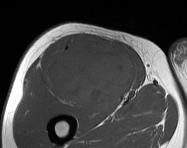
MRI of an extremity soft-tissue mass, one axial slice. Position 90 of 114 along the scan axis. MR volume resampled by the dataset authors to the PET/CT grid (not the native acquisition matrix). 3.27 mm slice thickness. 187 × 148 image matrix, field of view 183 × 145 mm. Male patient. From the clinical record (not read from this slice): histological type: pleiomorphic leiomyosarcoma; grade: intermediate; site of the primary tumour: right thigh.
Outlined on this slice (expert contour drawn on MRI and transferred to this co-registered scan by the dataset authors):
- gross tumour volume including surrounding oedema: box from (x=43, y=36) to (x=135, y=107) px
- gross tumour volume (mass): (x=45, y=36)–(x=135, y=107)